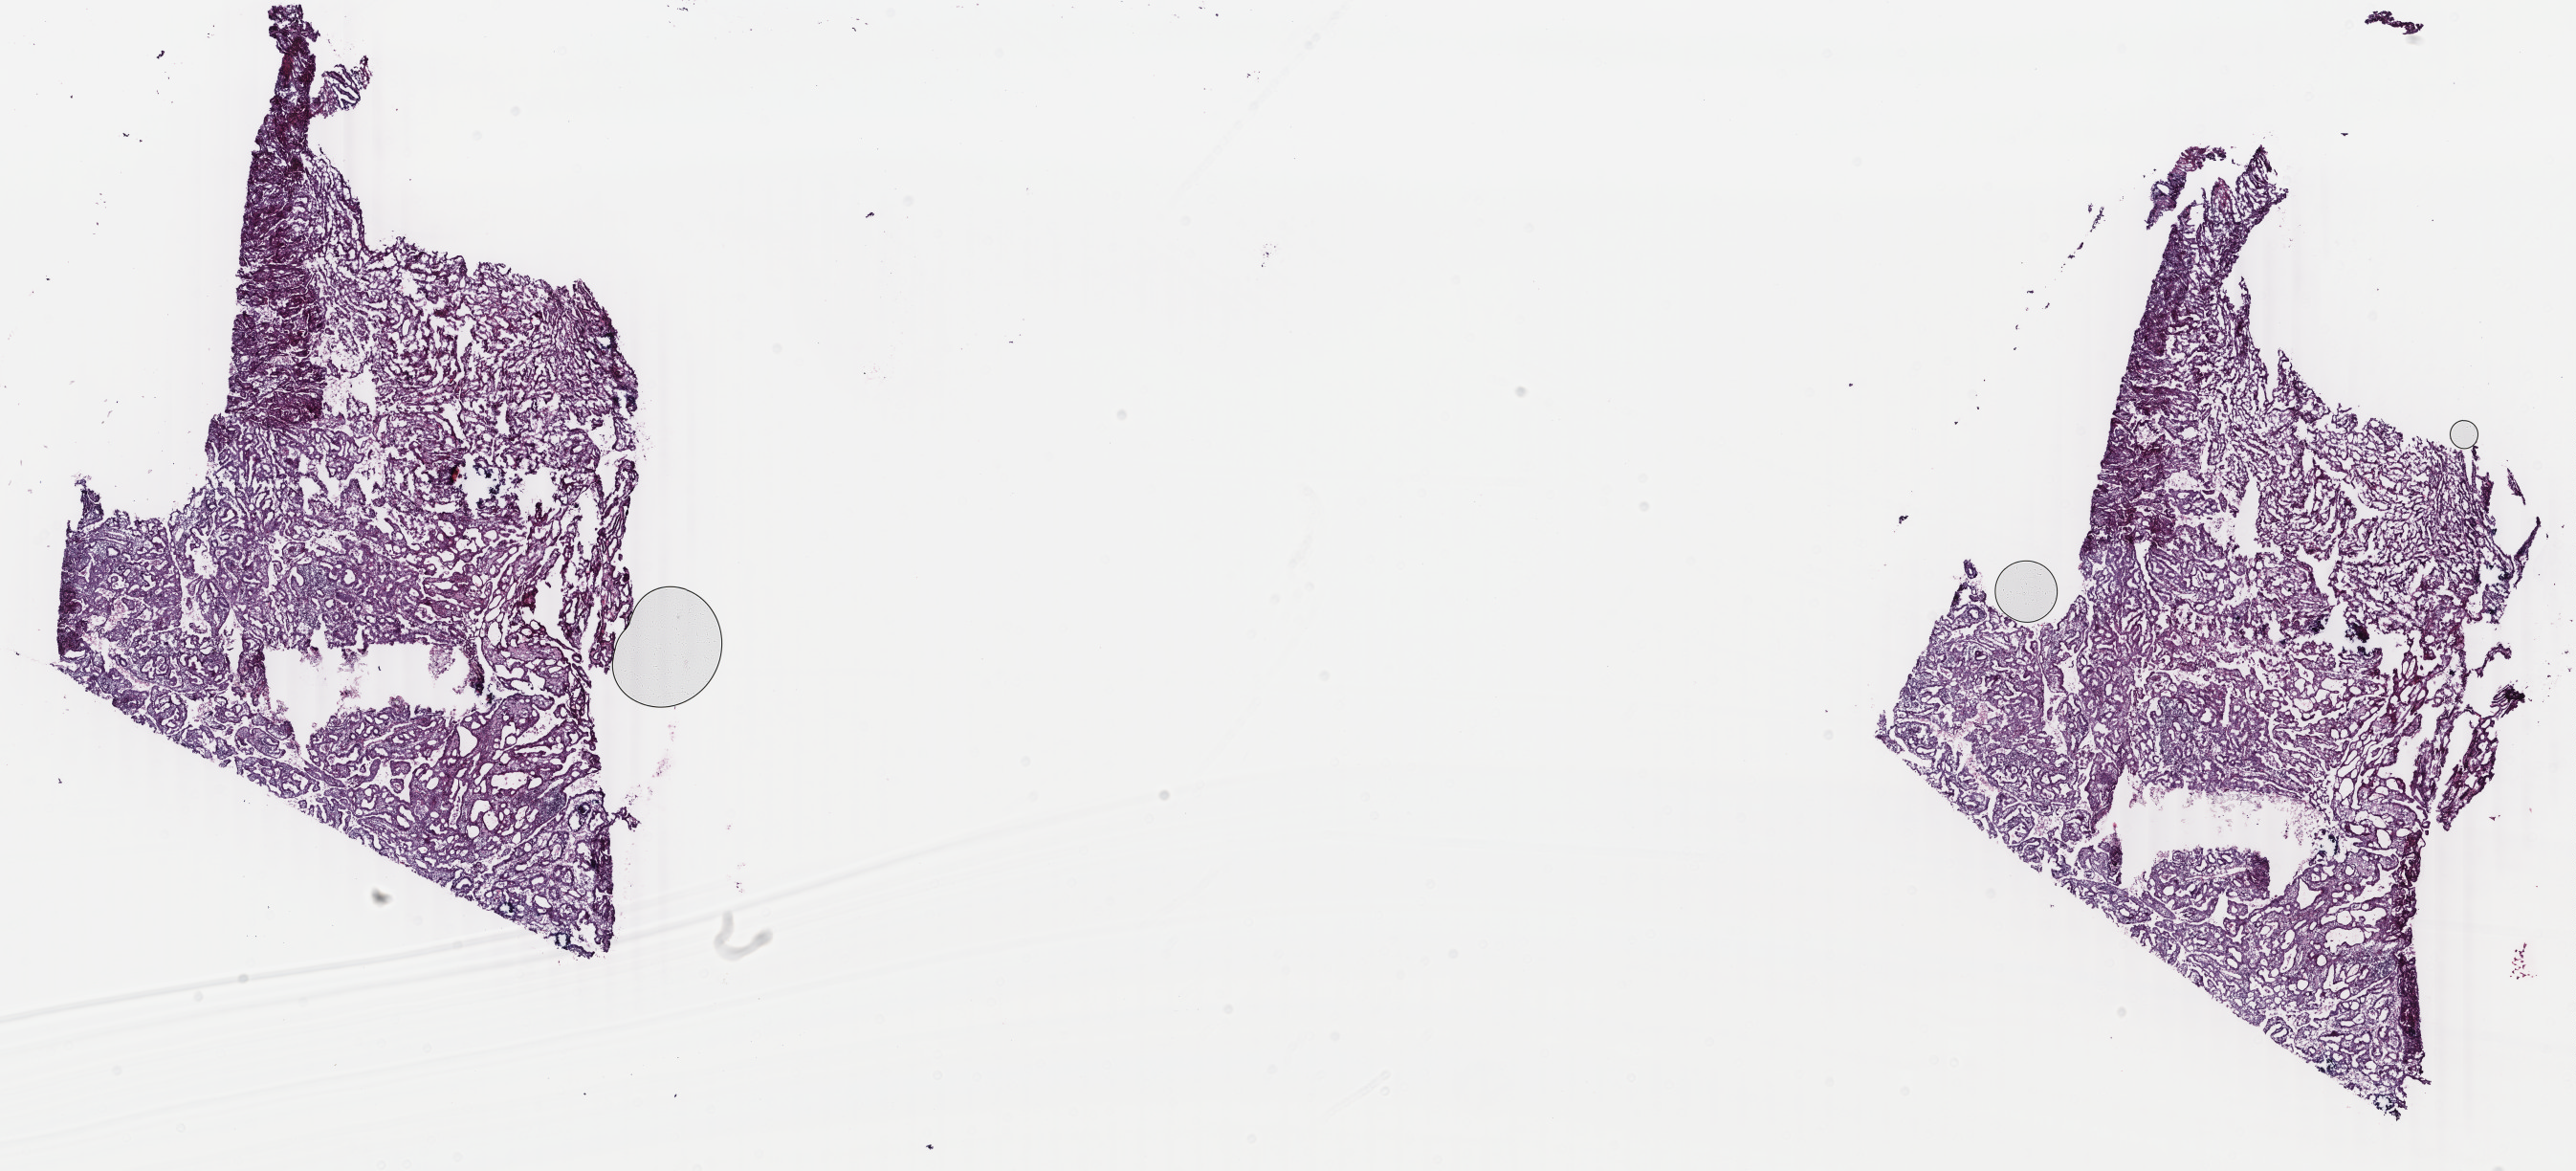
Digitized H&E-stained tissue section (whole slide) — low-resolution overview of the scanned area, about 21.4 x 9.7 mm (from a 40x scan). Frozen section from the bottom of the tissue portion. Primary tumour sample from the uterus. Female, age 58 years at initial diagnosis. Histologic grade: G2 (moderately differentiated). Composition of this section per pathologist review: tumour cells 70%, tumour nuclei 80%, normal cells 0%, stromal cells 20%, necrosis 10%. Infiltration values recorded for this section: lymphocyte infiltration 20%, monocyte infiltration 0%, neutrophil infiltration 20%.
* FIGO stage: IB
* diagnosis: Endometrioid adenocarcinoma, NOS (endometrium)
* lymph nodes positive (case pathology): 0 of 23 examined